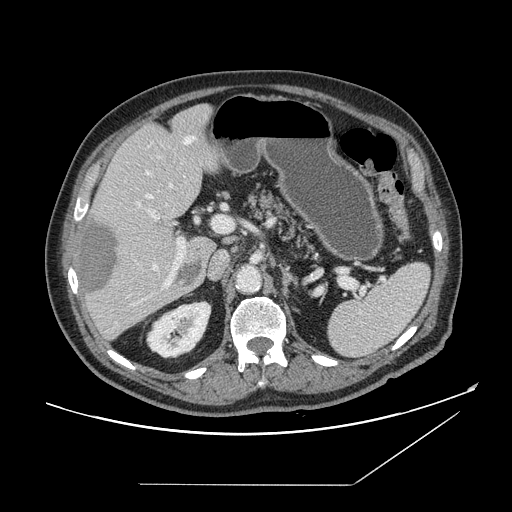
Contrast-enhanced abdominal CT, one axial slice; slice 93 of 166 in the series (ordered by position); 120 kVp; intravenous contrast given; soft-tissue window (W 400 / L 40 HU); 2.5 mm slice thickness; 512 × 512 image matrix. Male patient, age 80 years. Case-level facts recorded for this patient, not image findings: diagnosis: colorectal cancer liver metastases, imaged before liver resection; multiple liver metastases: no; largest metastasis: 2.2 cm; disease in both lobes: no.
Outlined on this slice (outlined manually by an expert reader):
- hepatic veins: box from (x=147, y=170) to (x=173, y=270) px
- liver: (x=76, y=105)–(x=222, y=340)
- planned liver remnant (the part of the liver to remain after resection): (x=95, y=105)–(x=222, y=252)
- portal vein (with intrahepatic branches): (x=138, y=202)–(x=231, y=285)
- liver metastasis: (x=79, y=222)–(x=201, y=294)